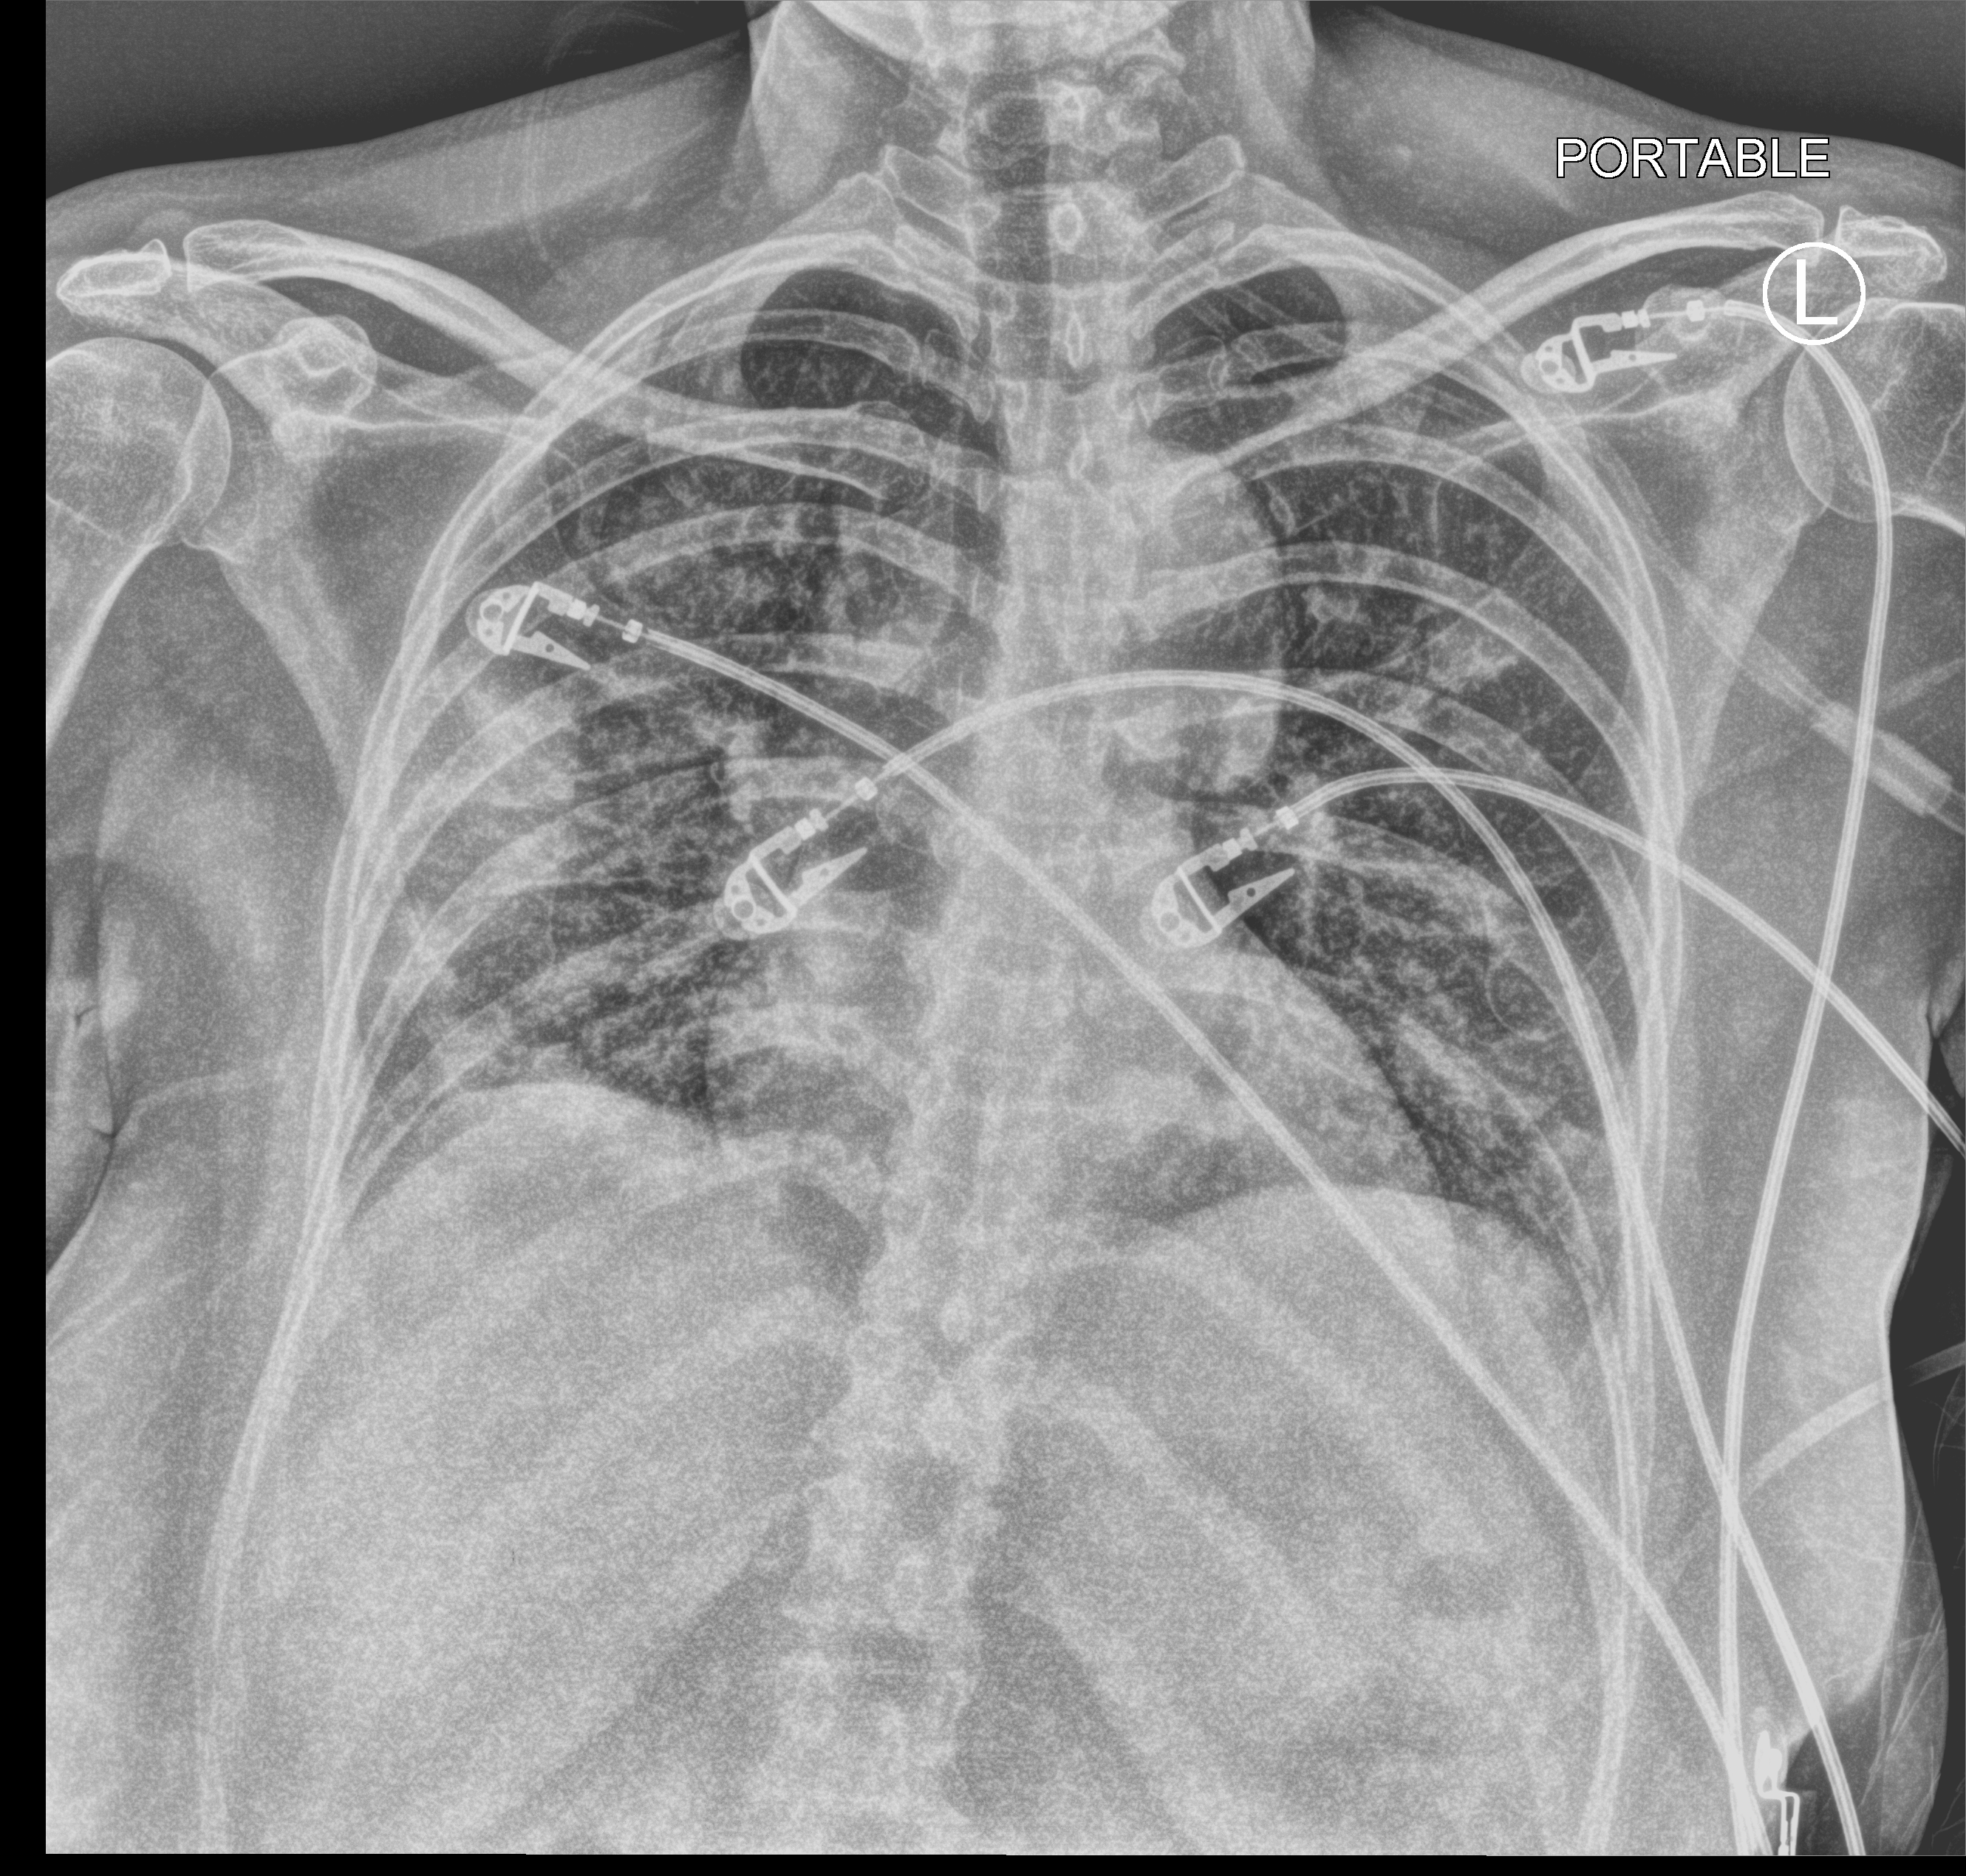
Portable chest radiograph; anteroposterior (AP) projection. Female patient hospitalised with COVID-19, age 18–59 years.
Admission-level facts for this patient (not findings on this image; timing relative to this image not recorded): mechanically ventilated during this hospital stay: yes; admitted to intensive care during this hospital stay: yes; COPD (admission record): no.